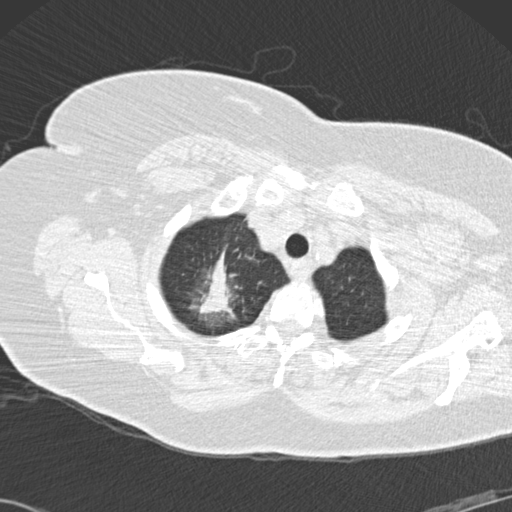
Low-dose screening chest CT, one axial slice. Position 128 of 146 along the scan axis. Reconstruction kernel B30f. 120 kVp. Lung window (W 1500 / L -600 HU). 512 × 512 image matrix, field of view 350 × 350 mm.
Annotated regions visible in this slice (outlined manually by an expert reader):
- lesion 1 (tumor, upper lobe of right lung): bounding box <190,251,234,317> (left, top, right, bottom; pixels)